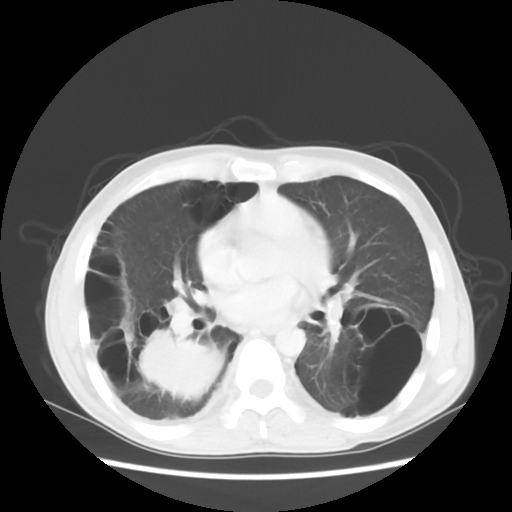
Chest CT, one axial slice; position 26 of 56 along the scan axis; 140 kVp; lung window (W 1500 / L -600 HU); 512 × 512 image matrix, field of view 351 × 351 mm. Male patient, age 41 years. Case-level facts recorded for this patient, not image findings: clinical TNM (as recorded): T4 N0 M1a; histopathological grade: G3.
Structures marked on this image (rectangle marked by the reading radiologist):
- lung tumour (recorded histology: large cell carcinoma): bounding box <137,327,229,401> (left, top, right, bottom; pixels)